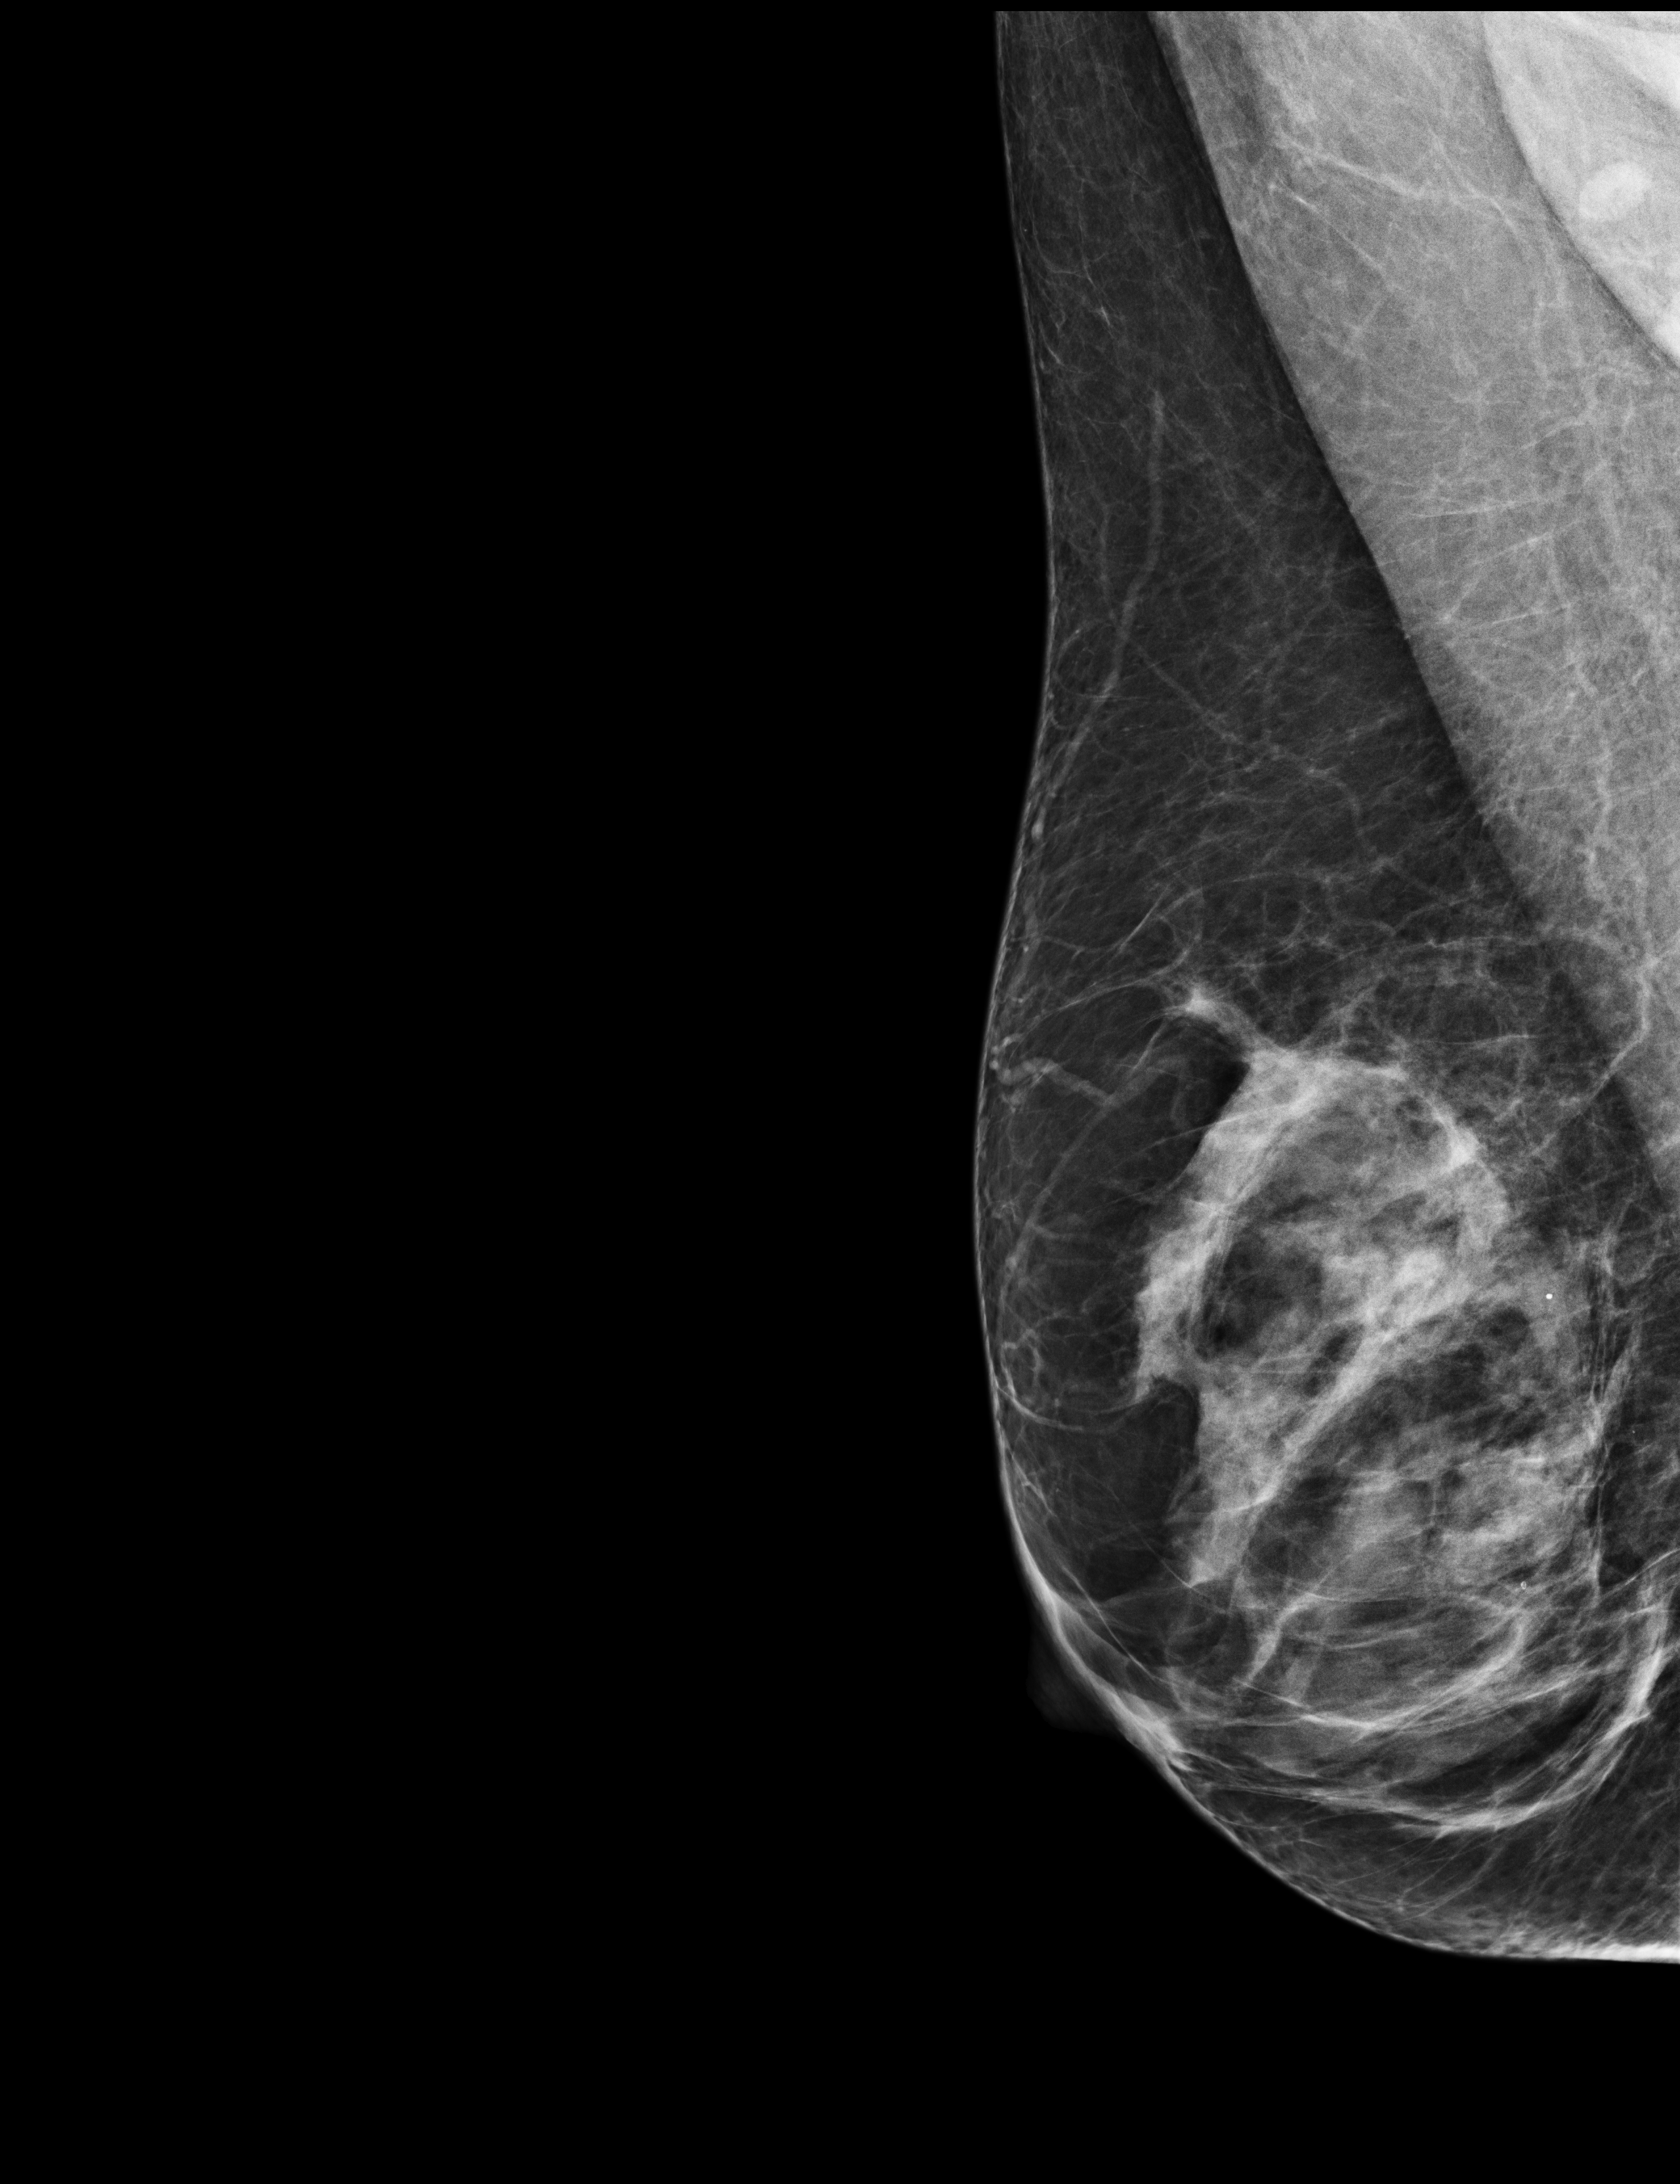
Screening examination, compressed breast thickness 61 mm. Patient: female, 59 years.
Image type: full-field digital mammogram. Breast: right. Projection: MLO view.